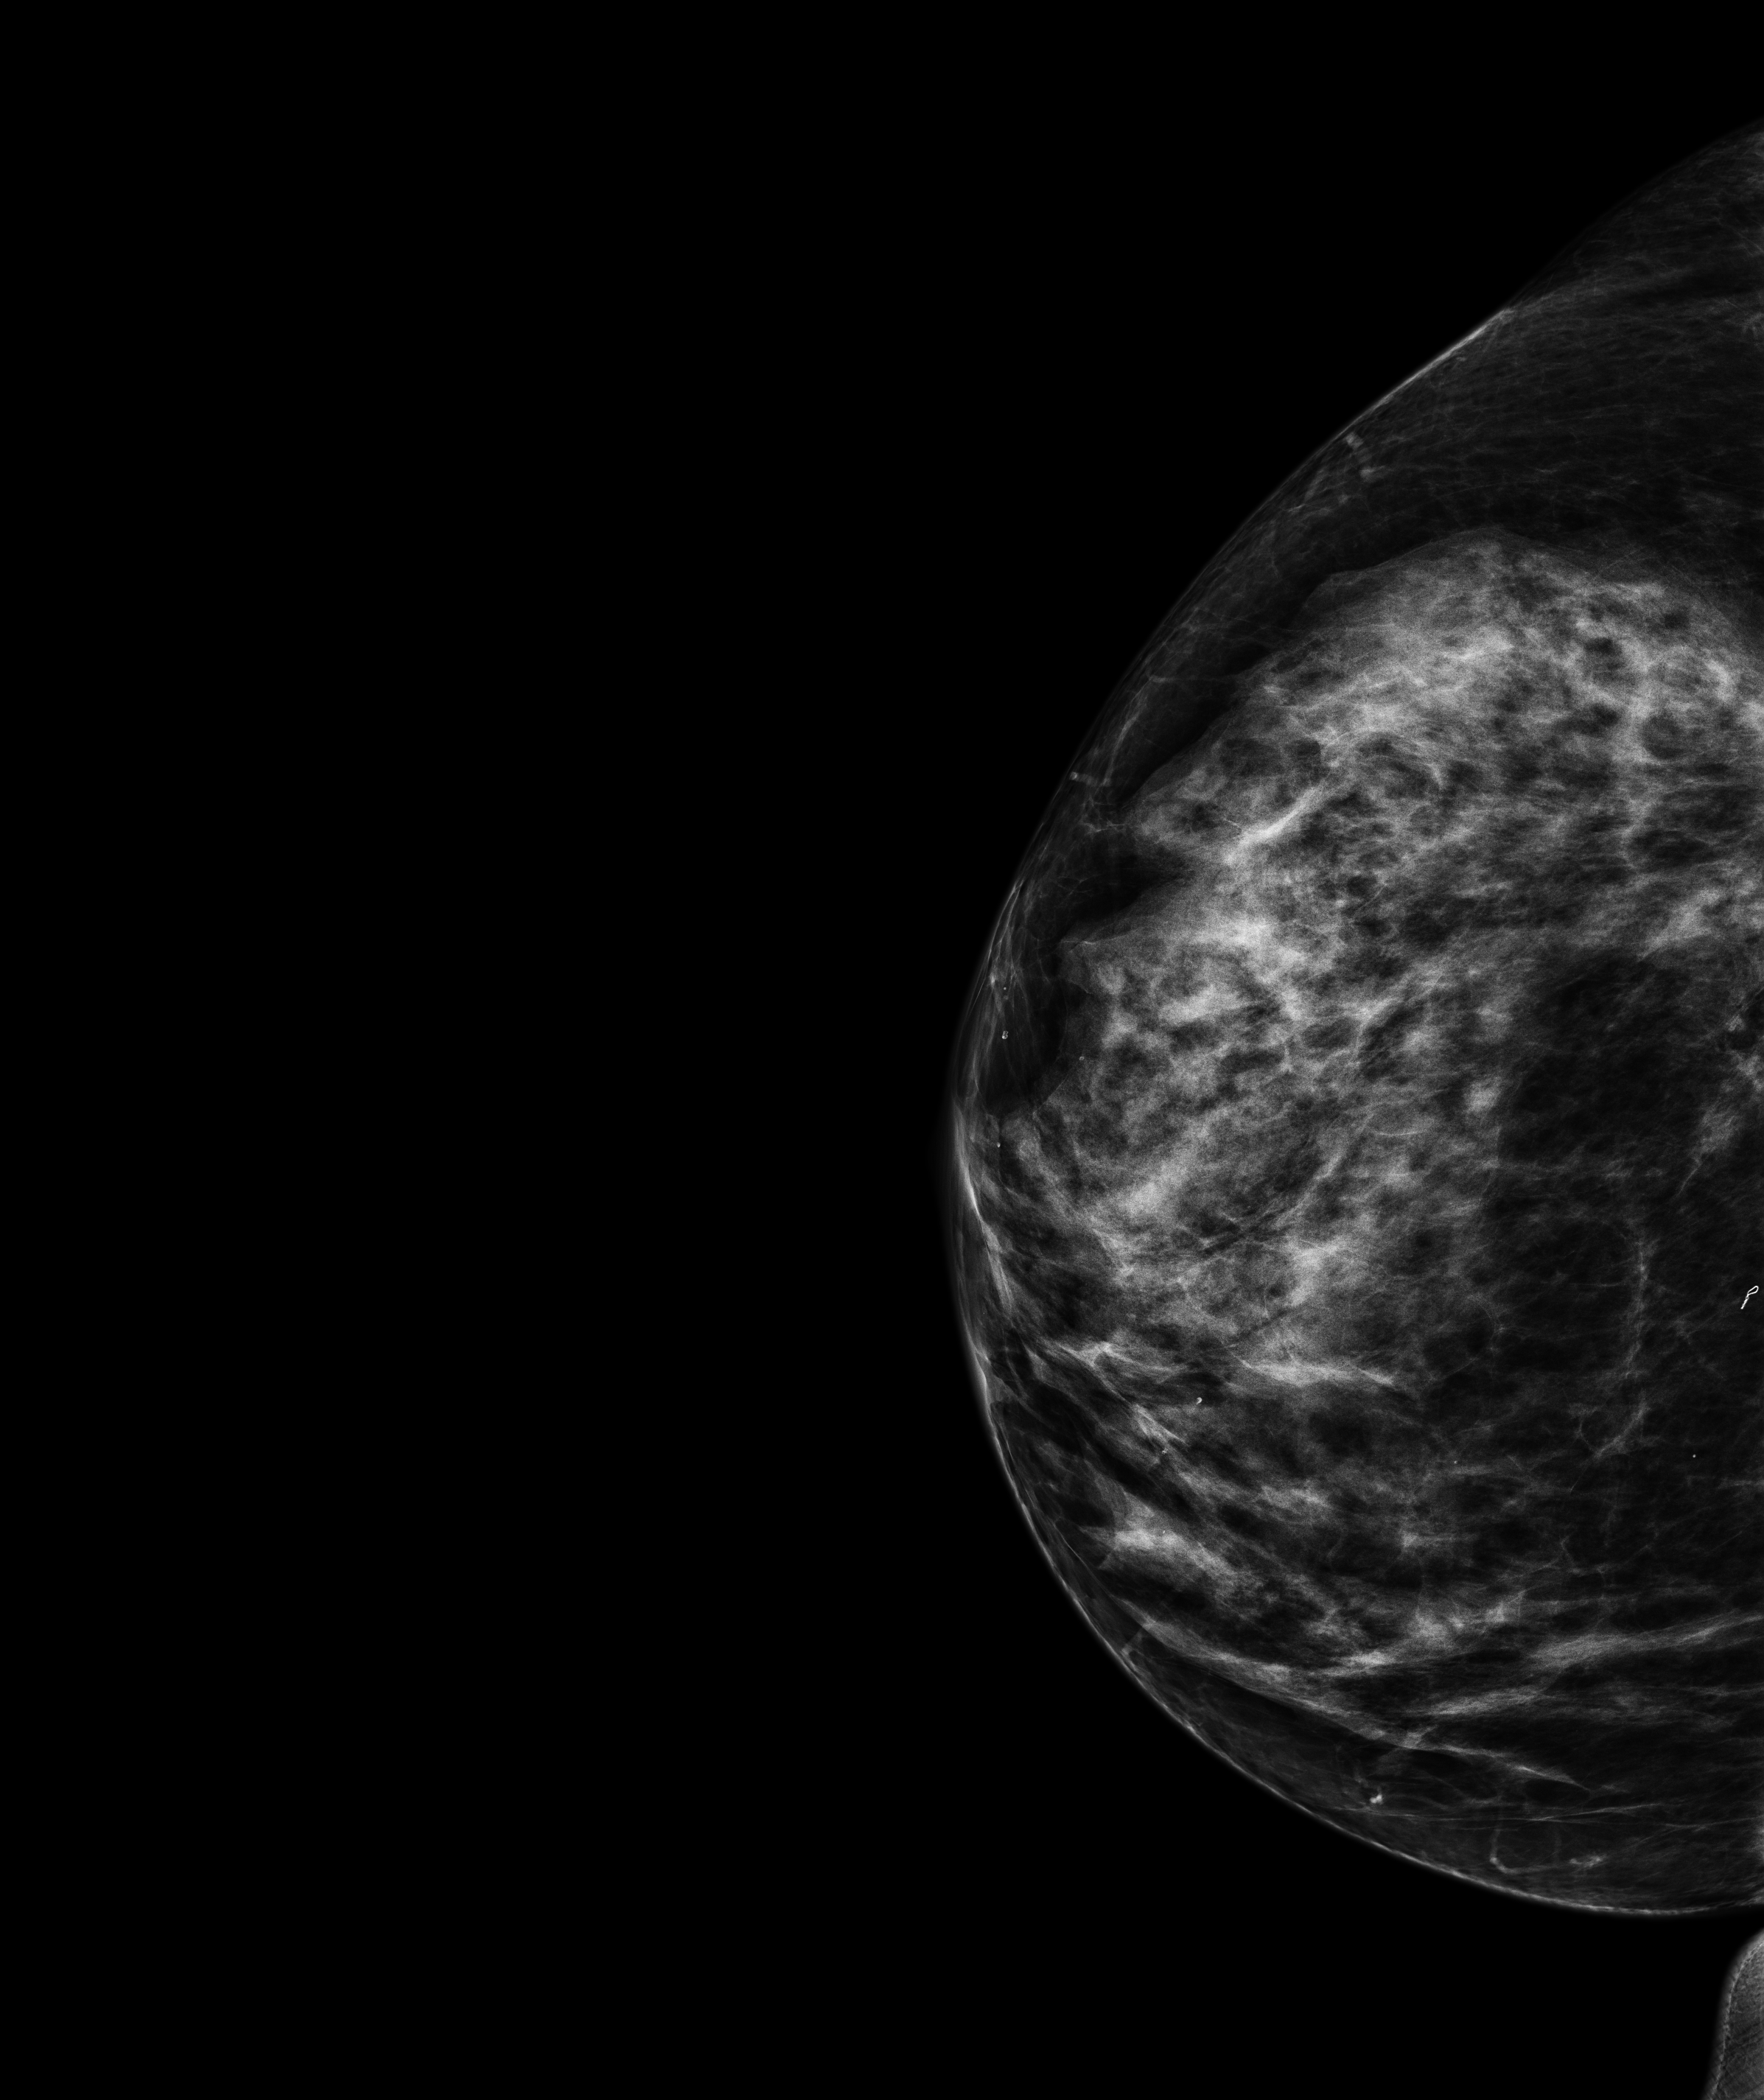
Annual screening mammography examination, compressed breast thickness 65.6 mm, system: Senographe Pristina. Patient aged 65 years (female).
Image type: full-field digital mammogram. Breast: right. Projection: craniocaudal (CC) view.